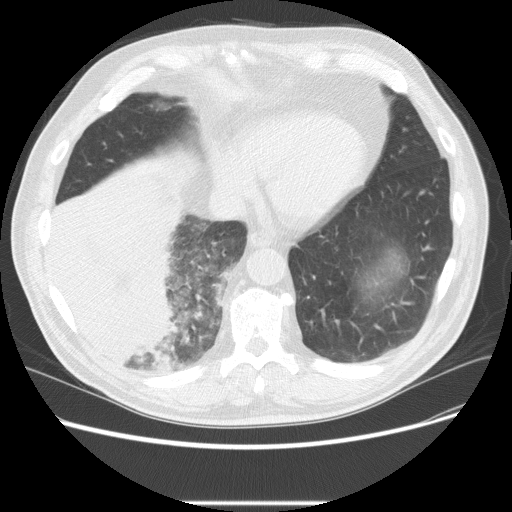
Low-dose screening chest CT, one axial slice. Position 63 of 233 along the scan axis. Lung window (W 1500 / L -600 HU). 2.5 mm slice thickness. 512 × 512 image matrix, field of view 380 × 380 mm.
Structures marked on this image (outlined manually by an expert reader):
- lesion 3 (tumor, lower lobe of right lung): box from (x=48, y=195) to (x=180, y=367) px